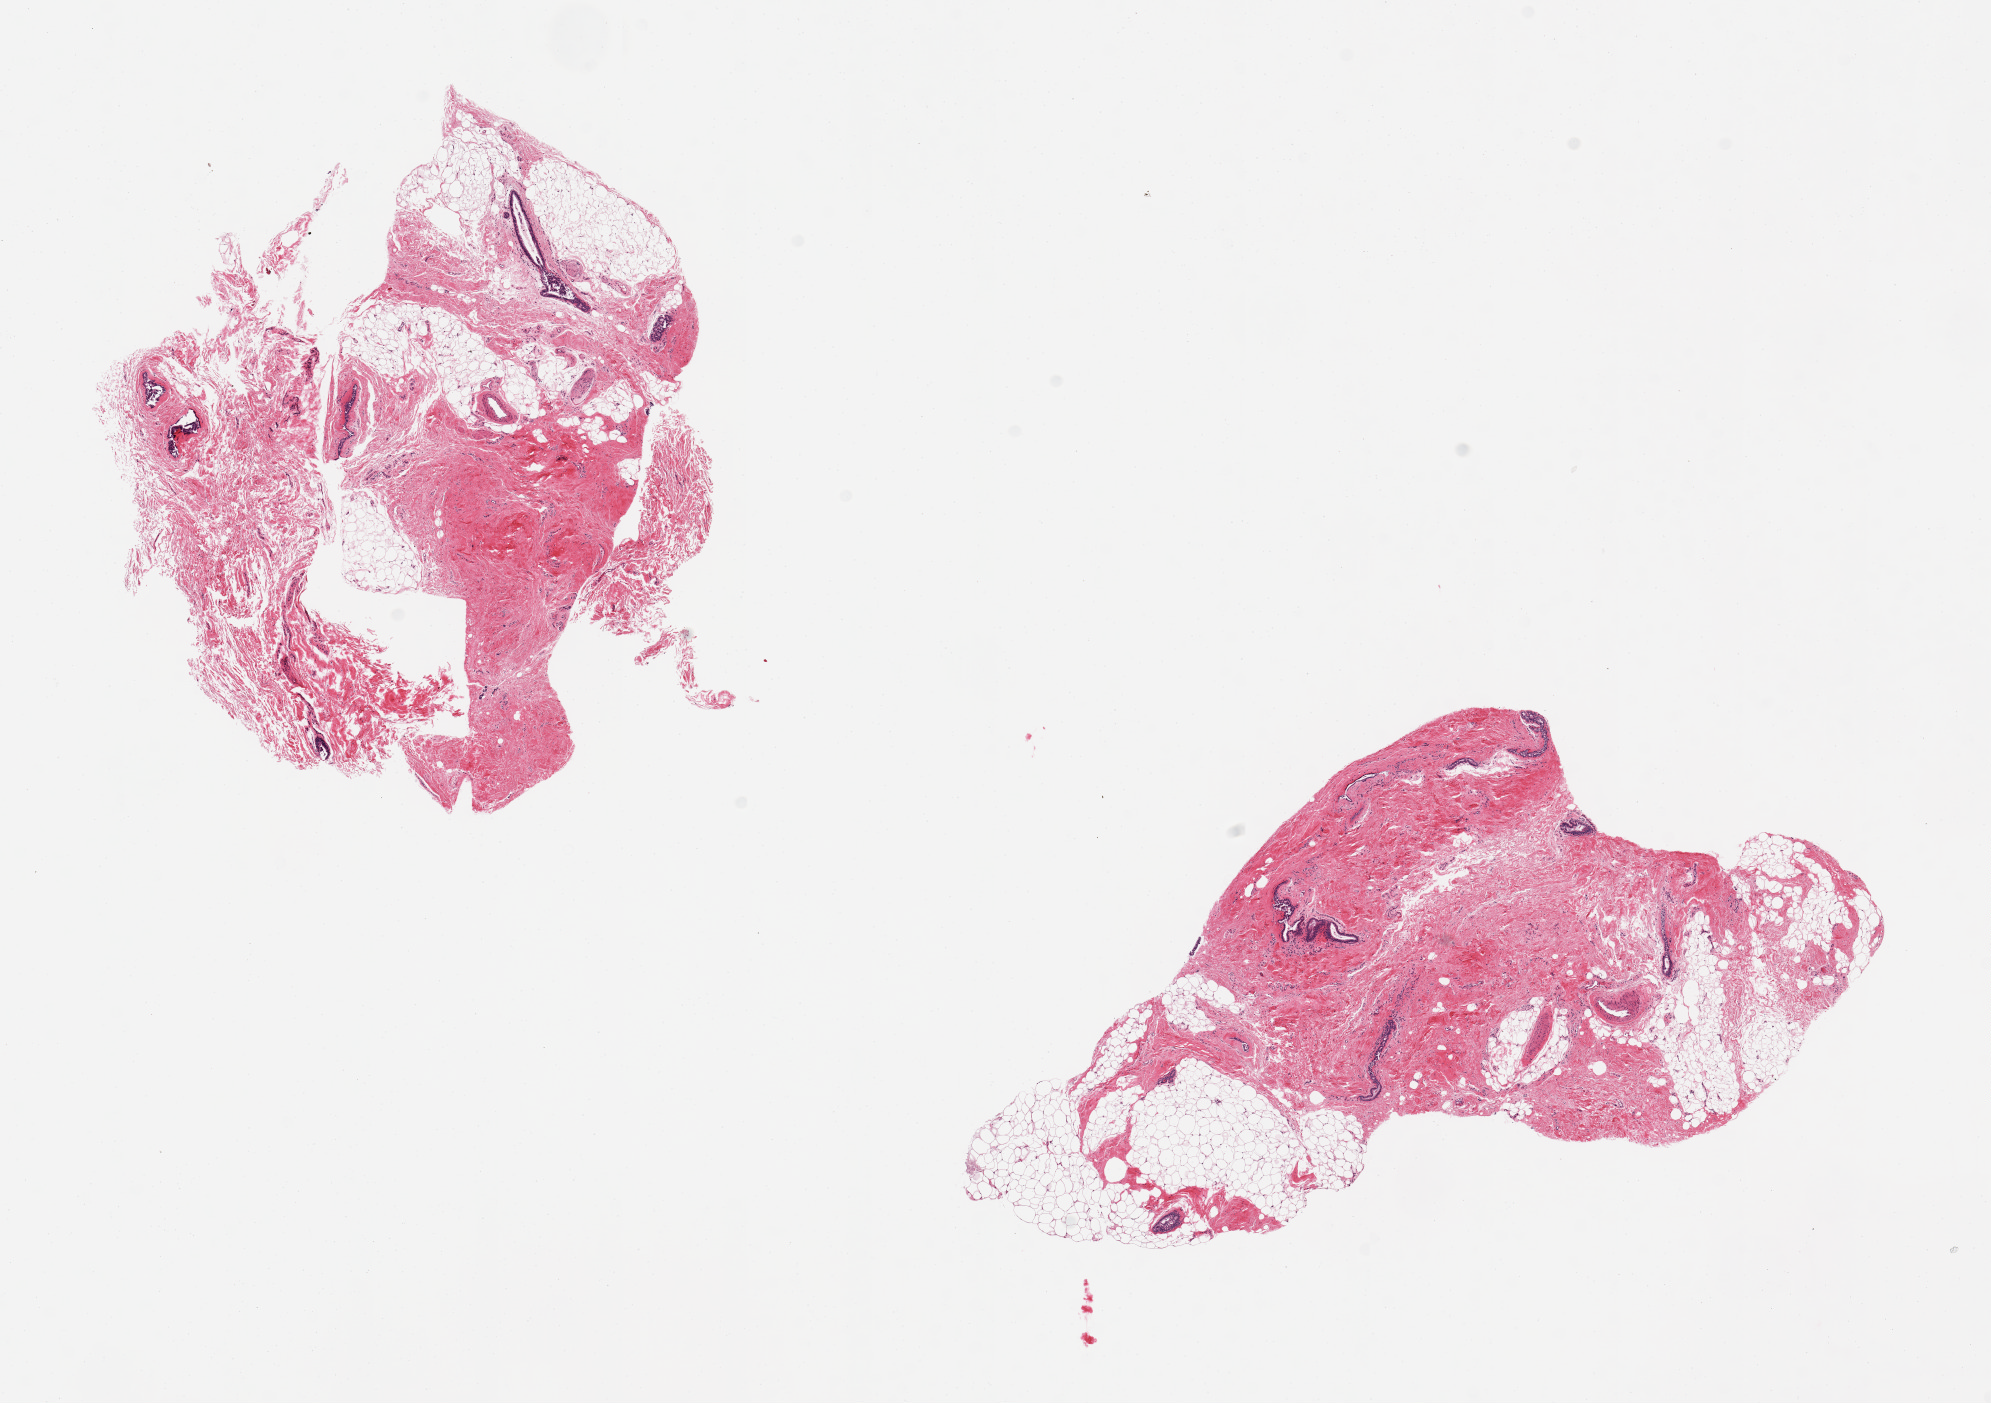
Whole-slide image, haematoxylin and eosin stain, whole scanned area (about 15.8 x 11.1 mm, slide scanned at 20x) shown as a low-resolution overview, PAXgene-fixed paraffin-embedded (PFPE) section, sampled site (target tissue): breast, donor tissue sample. Donor sex: male.
Pathologist's review note for this sample: 2 pieces gynecomastoid stromal (predominantly) hyperplasia; few ductal elements present.